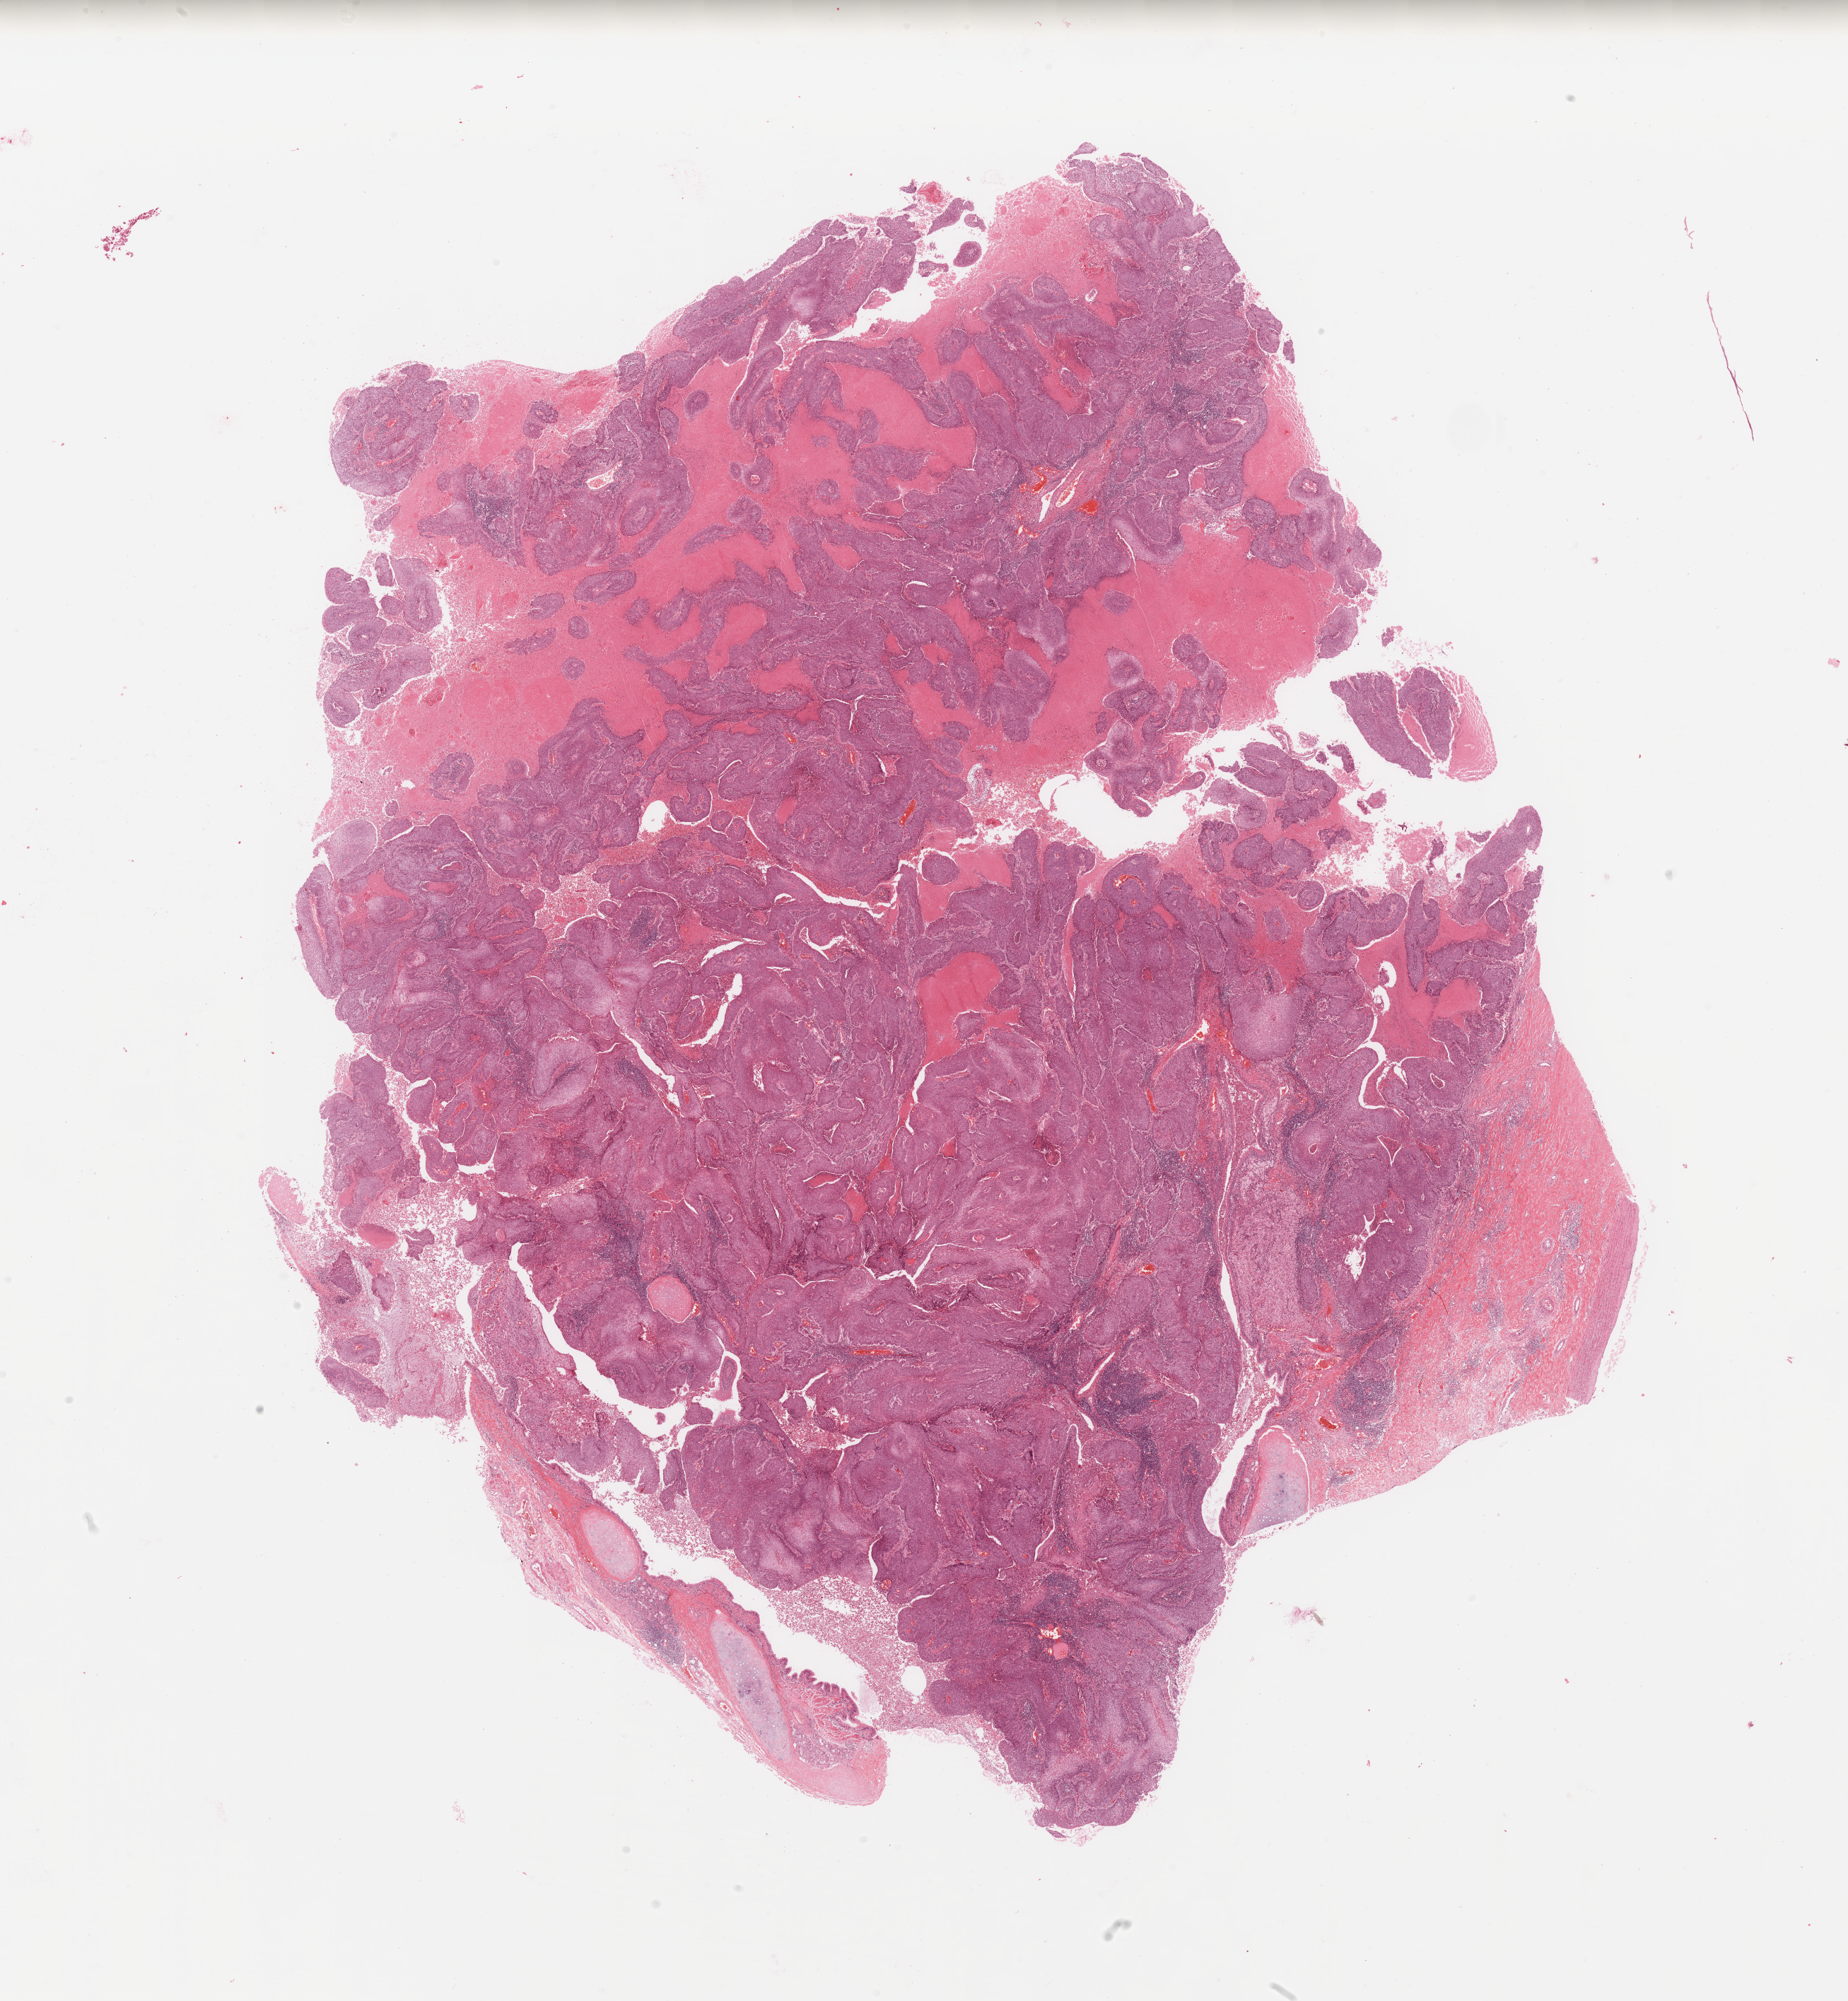
Whole-slide histology image, H&E-stained, whole scanned area (about 20.7 x 22.4 mm, from a 20x scan) shown as a low-resolution overview; tumour tissue sample, lung. 64-year-old male patient. Histologic grade: G3 (poorly differentiated).
AJCC pathologic stage: IB. Histologic diagnosis: Squamous cell carcinoma, NOS.